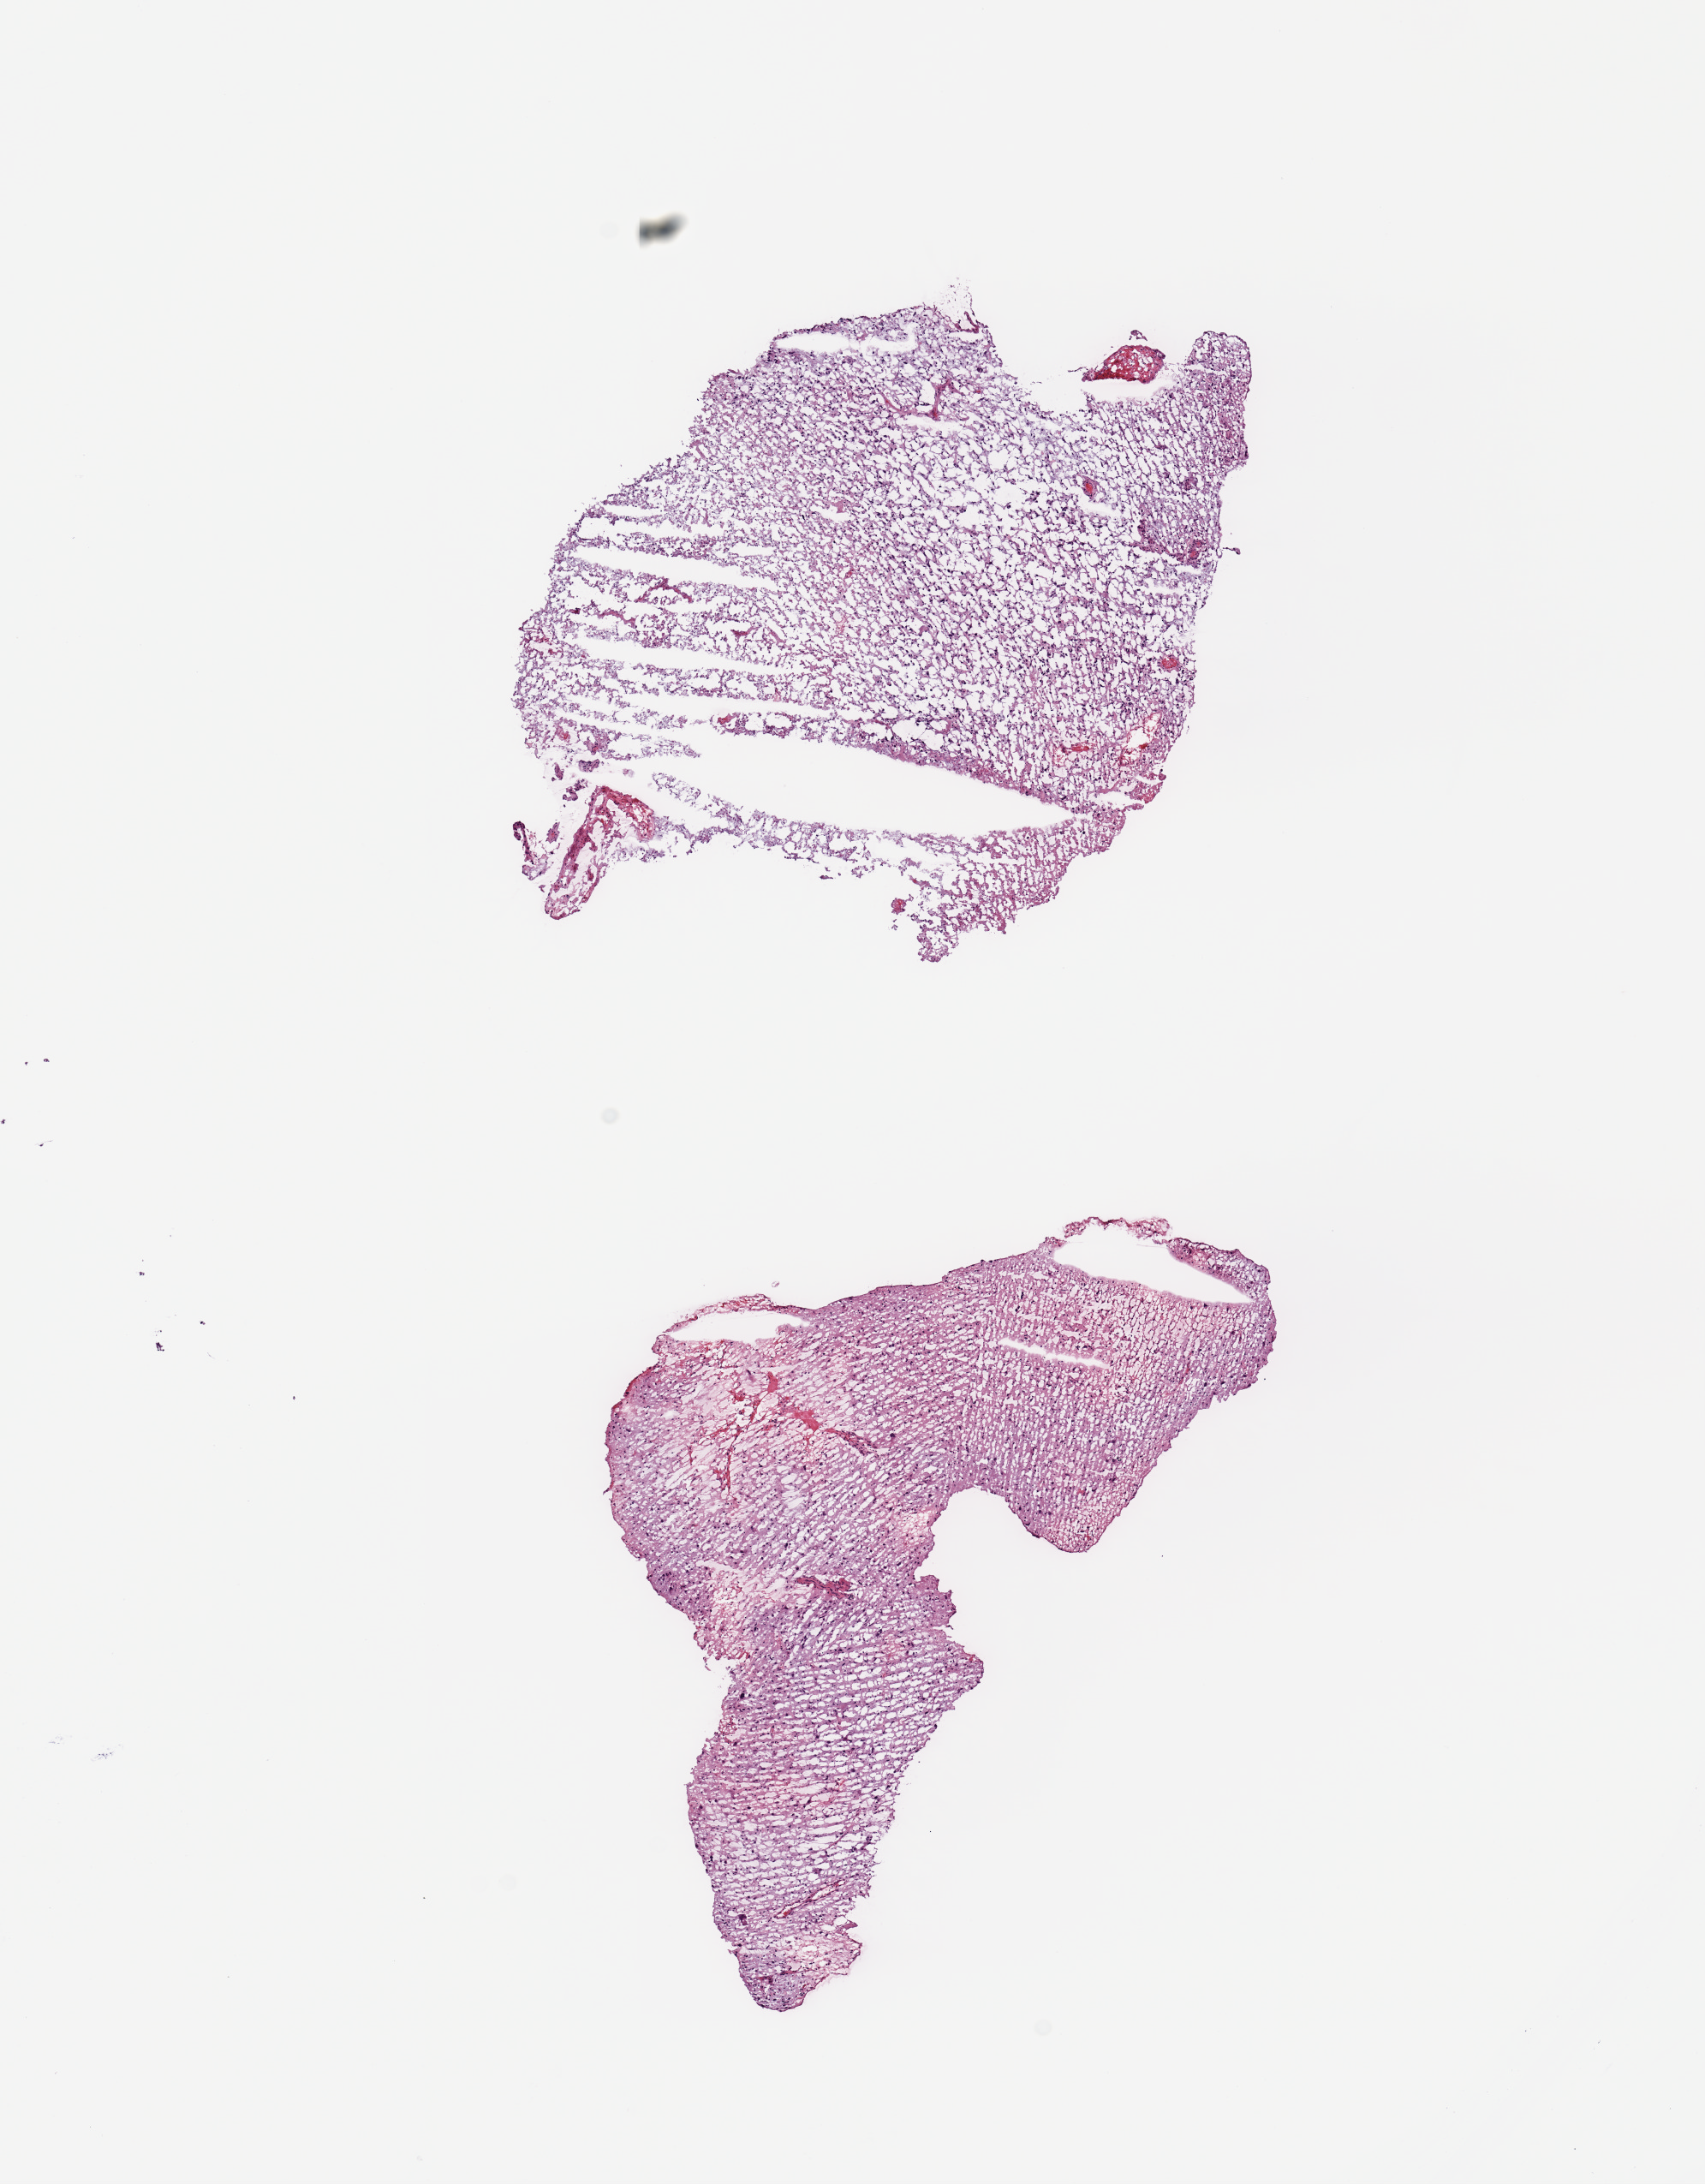
Digitized H&E tissue section (whole slide), whole scanned area (about 7.9 x 10.1 mm, from a 20x scan) shown as a low-resolution overview. Tumour tissue sample, brain. Female, 57 y/o.
Patient diagnosis (cohort enrolment): glioblastoma multiforme (brain). Primary tumour site (as recorded): temporal lobe.